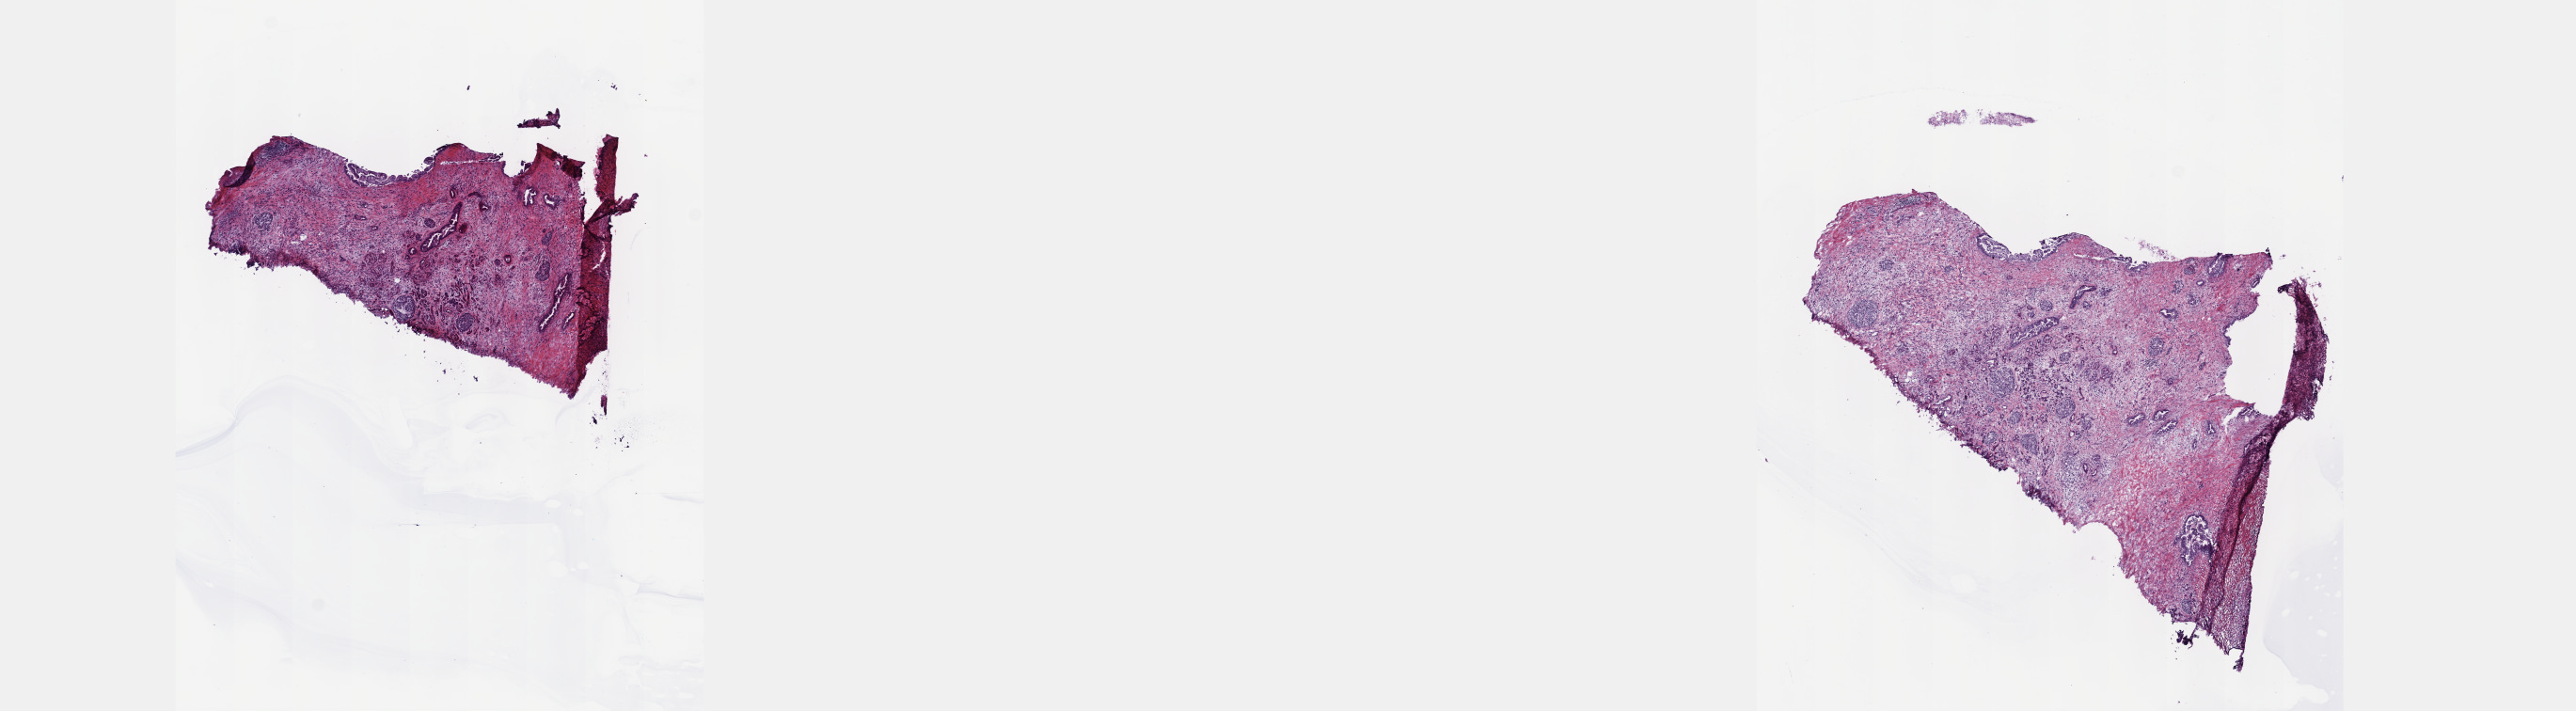
Digitized Hematoxylin and eosin (H&E) stained tissue section (whole slide), a low-resolution overview of the entire scanned area, about 22.1 x 6.1 mm (acquisition: 40x scan). Frozen section. Sample: primary tumour, pancreas. Female, age 77 years at initial diagnosis. Histologic grade: G3 (poorly differentiated). Composition of this section per pathologist review: tumour cells 10%, tumour nuclei 20%, normal cells 20%, stromal cells 70%, necrosis 0%. Infiltration values recorded for this section: lymphocyte infiltration 0%, monocyte infiltration 0%, neutrophil infiltration 0%.
AJCC pathologic stage: IIB (7th edition). Histologic diagnosis: Infiltrating duct carcinoma, NOS (head of pancreas).